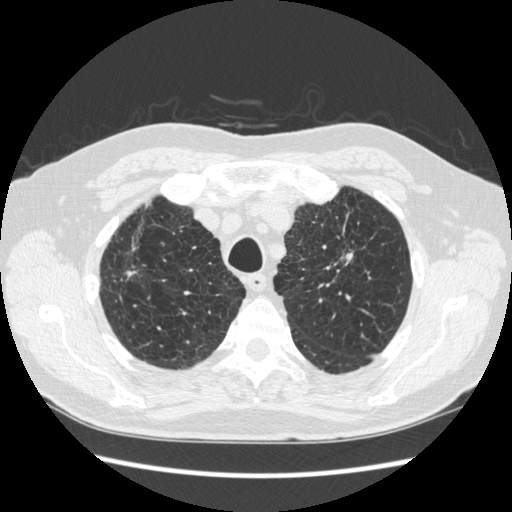
Axial slice from a low-dose chest CT screening exam. Third annual screen. Lung window (W 1500 / L -600 HU). Standard (soft-tissue) reconstruction kernel (STANDARD). 512 × 512 image matrix. Male, age 70 years at enrolment.
• Expert reader's lesion annotation, bounding box (x1, y1, x2, y2) in pixels: (322, 213, 371, 277).
• The screening reader recorded 2 non-calcified nodules or masses ≥4 mm on this exam (left upper lobe, right lower lobe); which of them this box marks is not recorded.
• Lung cancer was diagnosed 92 days after this screen: squamous cell carcinoma, NOS, left upper lobe, moderately differentiated (G2), stage IA (AJCC 6th edition), 18 mm at pathology.